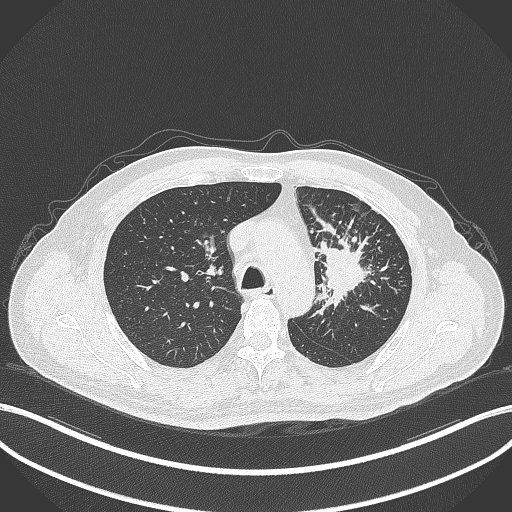
Chest CT, one axial slice. Slice 256 of 386 in the series (ordered by position). Reconstruction kernel B70f. 120 kVp. Lung window (W 1500 / L -600 HU). 1 mm slice thickness. 512 × 512 image matrix, field of view 400 × 400 mm. Male patient, age 69 years. Case-level facts recorded for this patient, not image findings: clinical TNM (as recorded): T2a N2 M0; histopathological grade: G2-3.
Annotated regions visible in this slice (rectangle marked by the reading radiologist):
- lung tumour (recorded histology: adenocarcinoma): bounding box (x1, y1, x2, y2) in pixels: (316, 238, 371, 311)